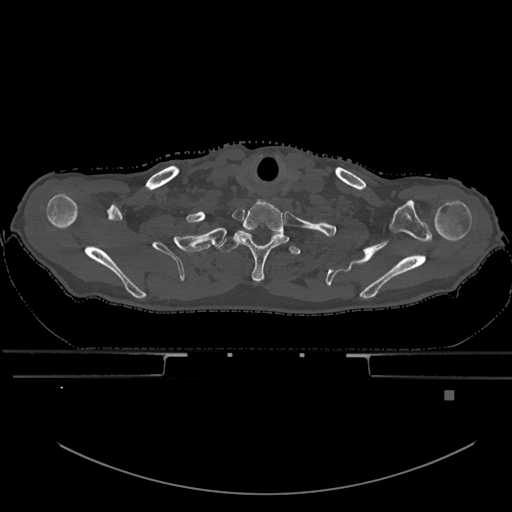
CT including the spine, one axial slice; bone window (W 1800 / L 400 HU); 0.5 mm slice thickness; 512 × 512 image matrix, field of view 456 × 456 mm. Male patient, age 82 years. Case-level facts recorded for this patient, not image findings: primary cancer: prostate; vertebrae with lytic lesions (as recorded): T11, T9, T8, T2.
Structures marked on this image (semi-automatic segmentation, software-assisted and operator-edited):
- T1 vertebra: bounding box [x1, y1, x2, y2] px = [218, 236, 301, 256]